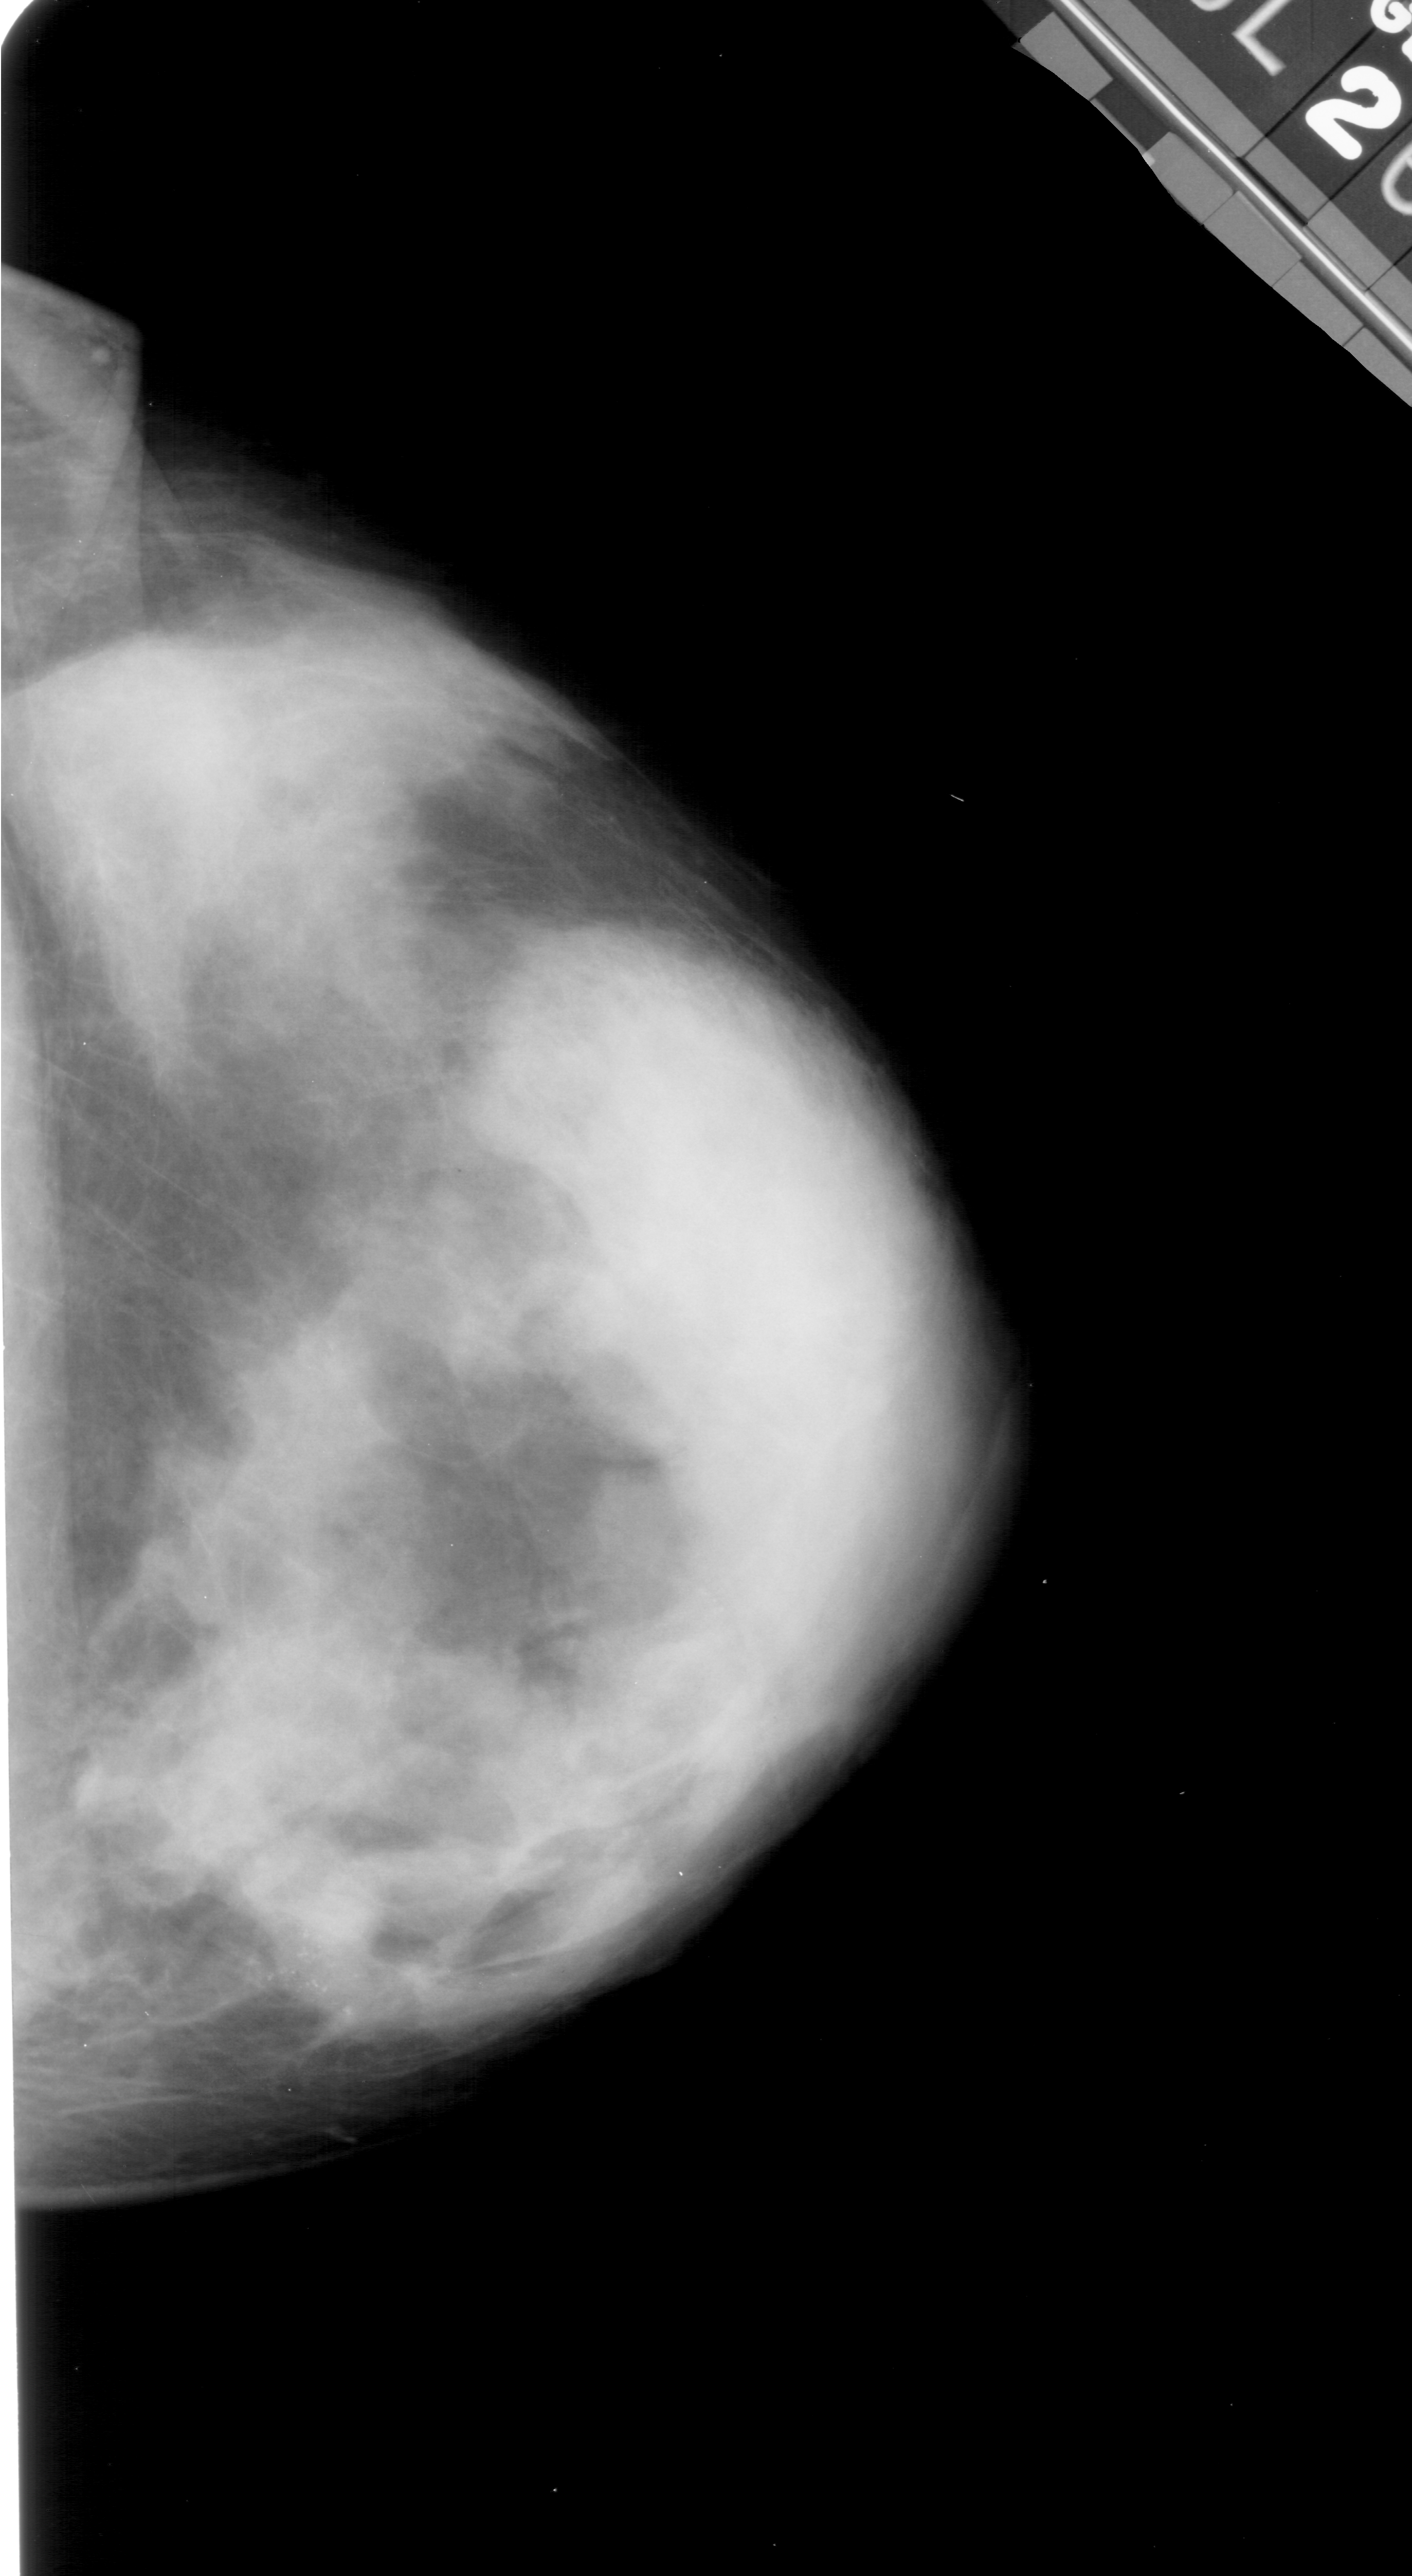
Scanned film-screen mammogram. Right breast. CC view. 1412 × 2576 image matrix.
Expert-marked regions of interest on this film, with their recorded descriptors:
- calcifications, morphology pleomorphic, distribution clustered; BI-RADS assessment category 4; subtlety rating 3 on a 1 (subtle) to 5 (obvious) scale; pathology result (as recorded, not read from the image): malignant: bounding box <278,1904,381,2035> (left, top, right, bottom; pixels)